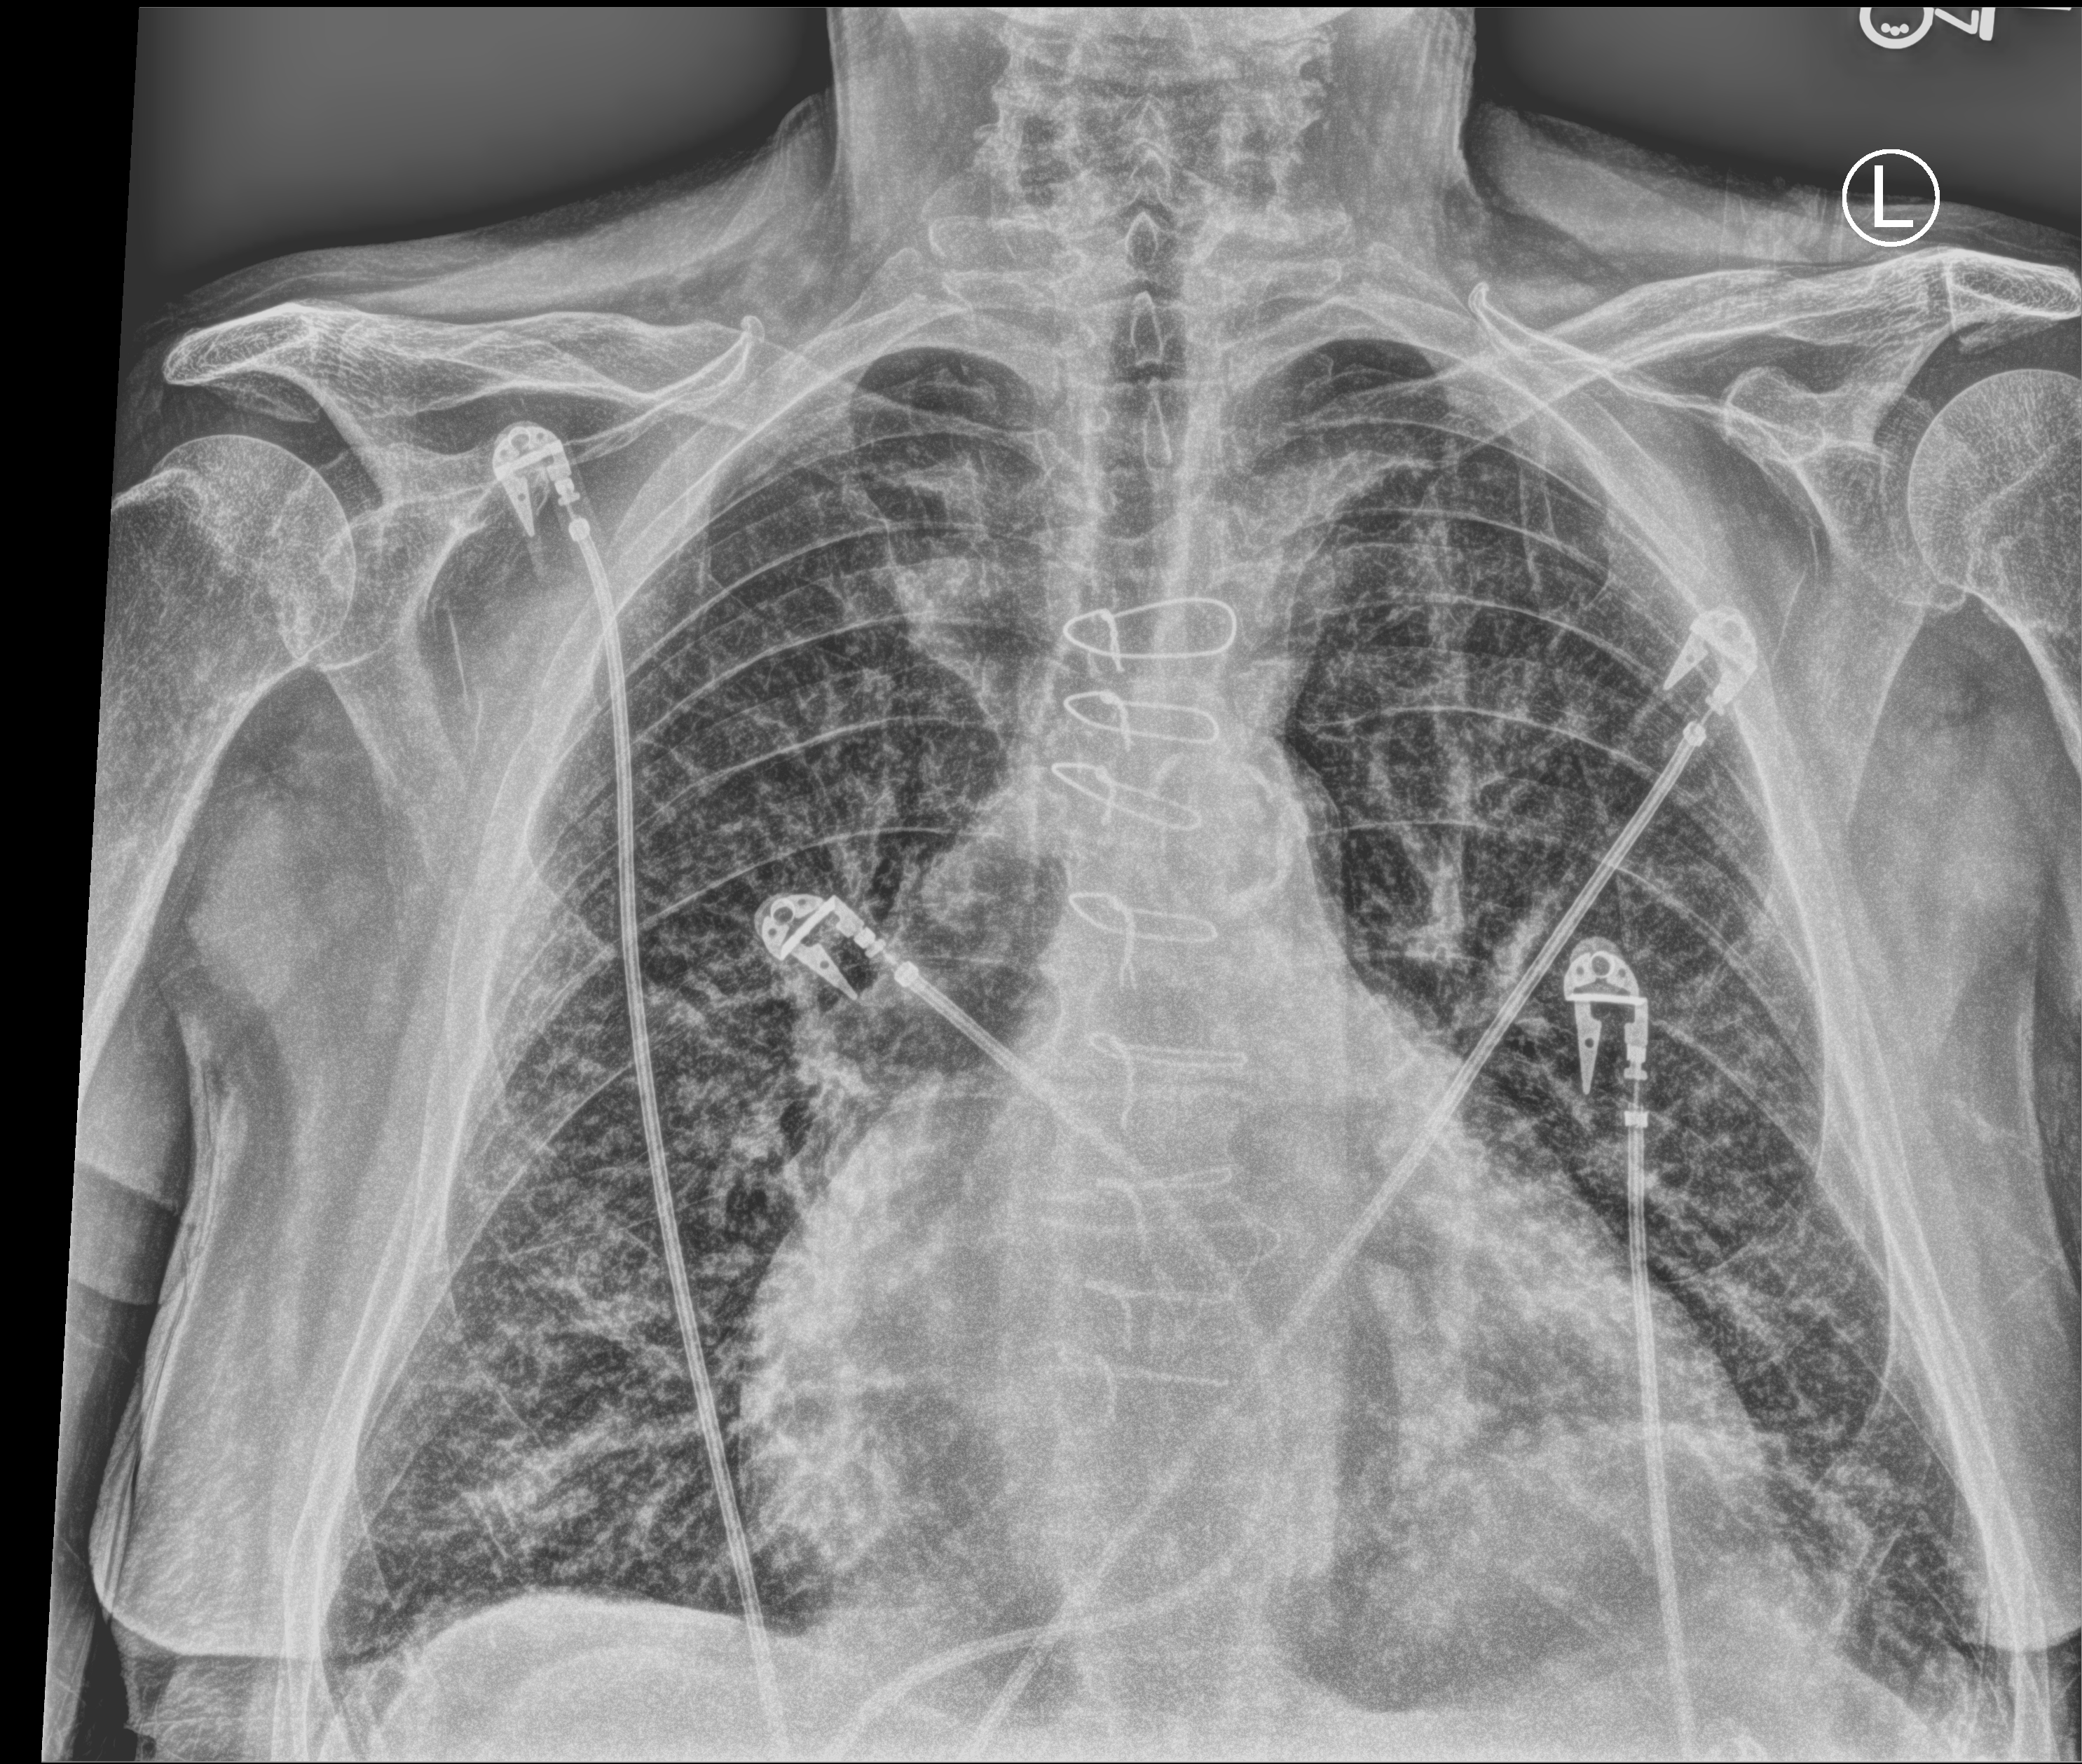
Chest X-ray (portable), anteroposterior (AP) projection. Patient hospitalised with COVID-19; male, aged 75–90 years.
Admission-level facts for this patient (not findings on this image; timing relative to this image not recorded): admitted to intensive care during this hospital stay: yes.